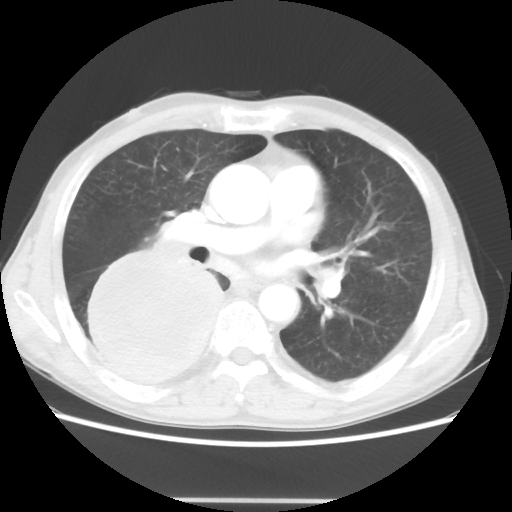
Chest CT, one axial slice. Position 25 of 48 along the scan axis. Lung window (W 1500 / L -600 HU). 5 mm slice thickness. 512 × 512 image matrix, field of view 361 × 361 mm. Patient: male, 66 years. Case-level facts recorded for this patient, not image findings: clinical TNM (as recorded): T4 N1 M1.
Annotated regions visible in this slice (rectangle marked by the reading radiologist):
- lung tumour (recorded histology: small cell carcinoma): bounding box <75,240,234,388> (left, top, right, bottom; pixels)